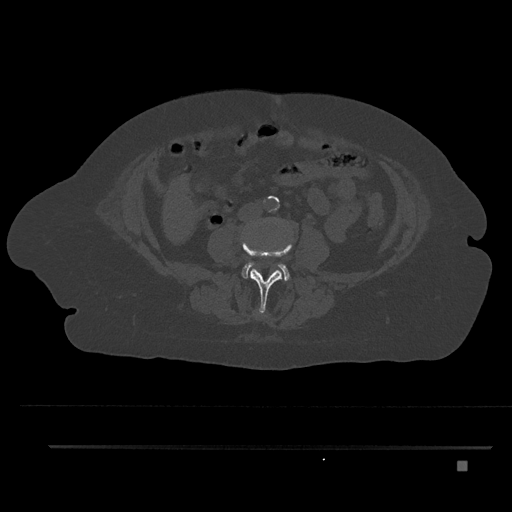
CT including the spine, one axial slice. 120 kVp. Bone window (W 1800 / L 400 HU). 512 × 512 image matrix, field of view 437 × 437 mm. Patient: female, 76 years. From the clinical record (not read from this slice): primary cancer: lung.
Annotated regions visible in this slice (semi-automatically segmented with operator editing):
- L2 vertebra: box from (x=259, y=312) to (x=262, y=315) px
- L3 vertebra: (x=242, y=233)–(x=293, y=313)
- L4 vertebra: (x=242, y=237)–(x=290, y=281)